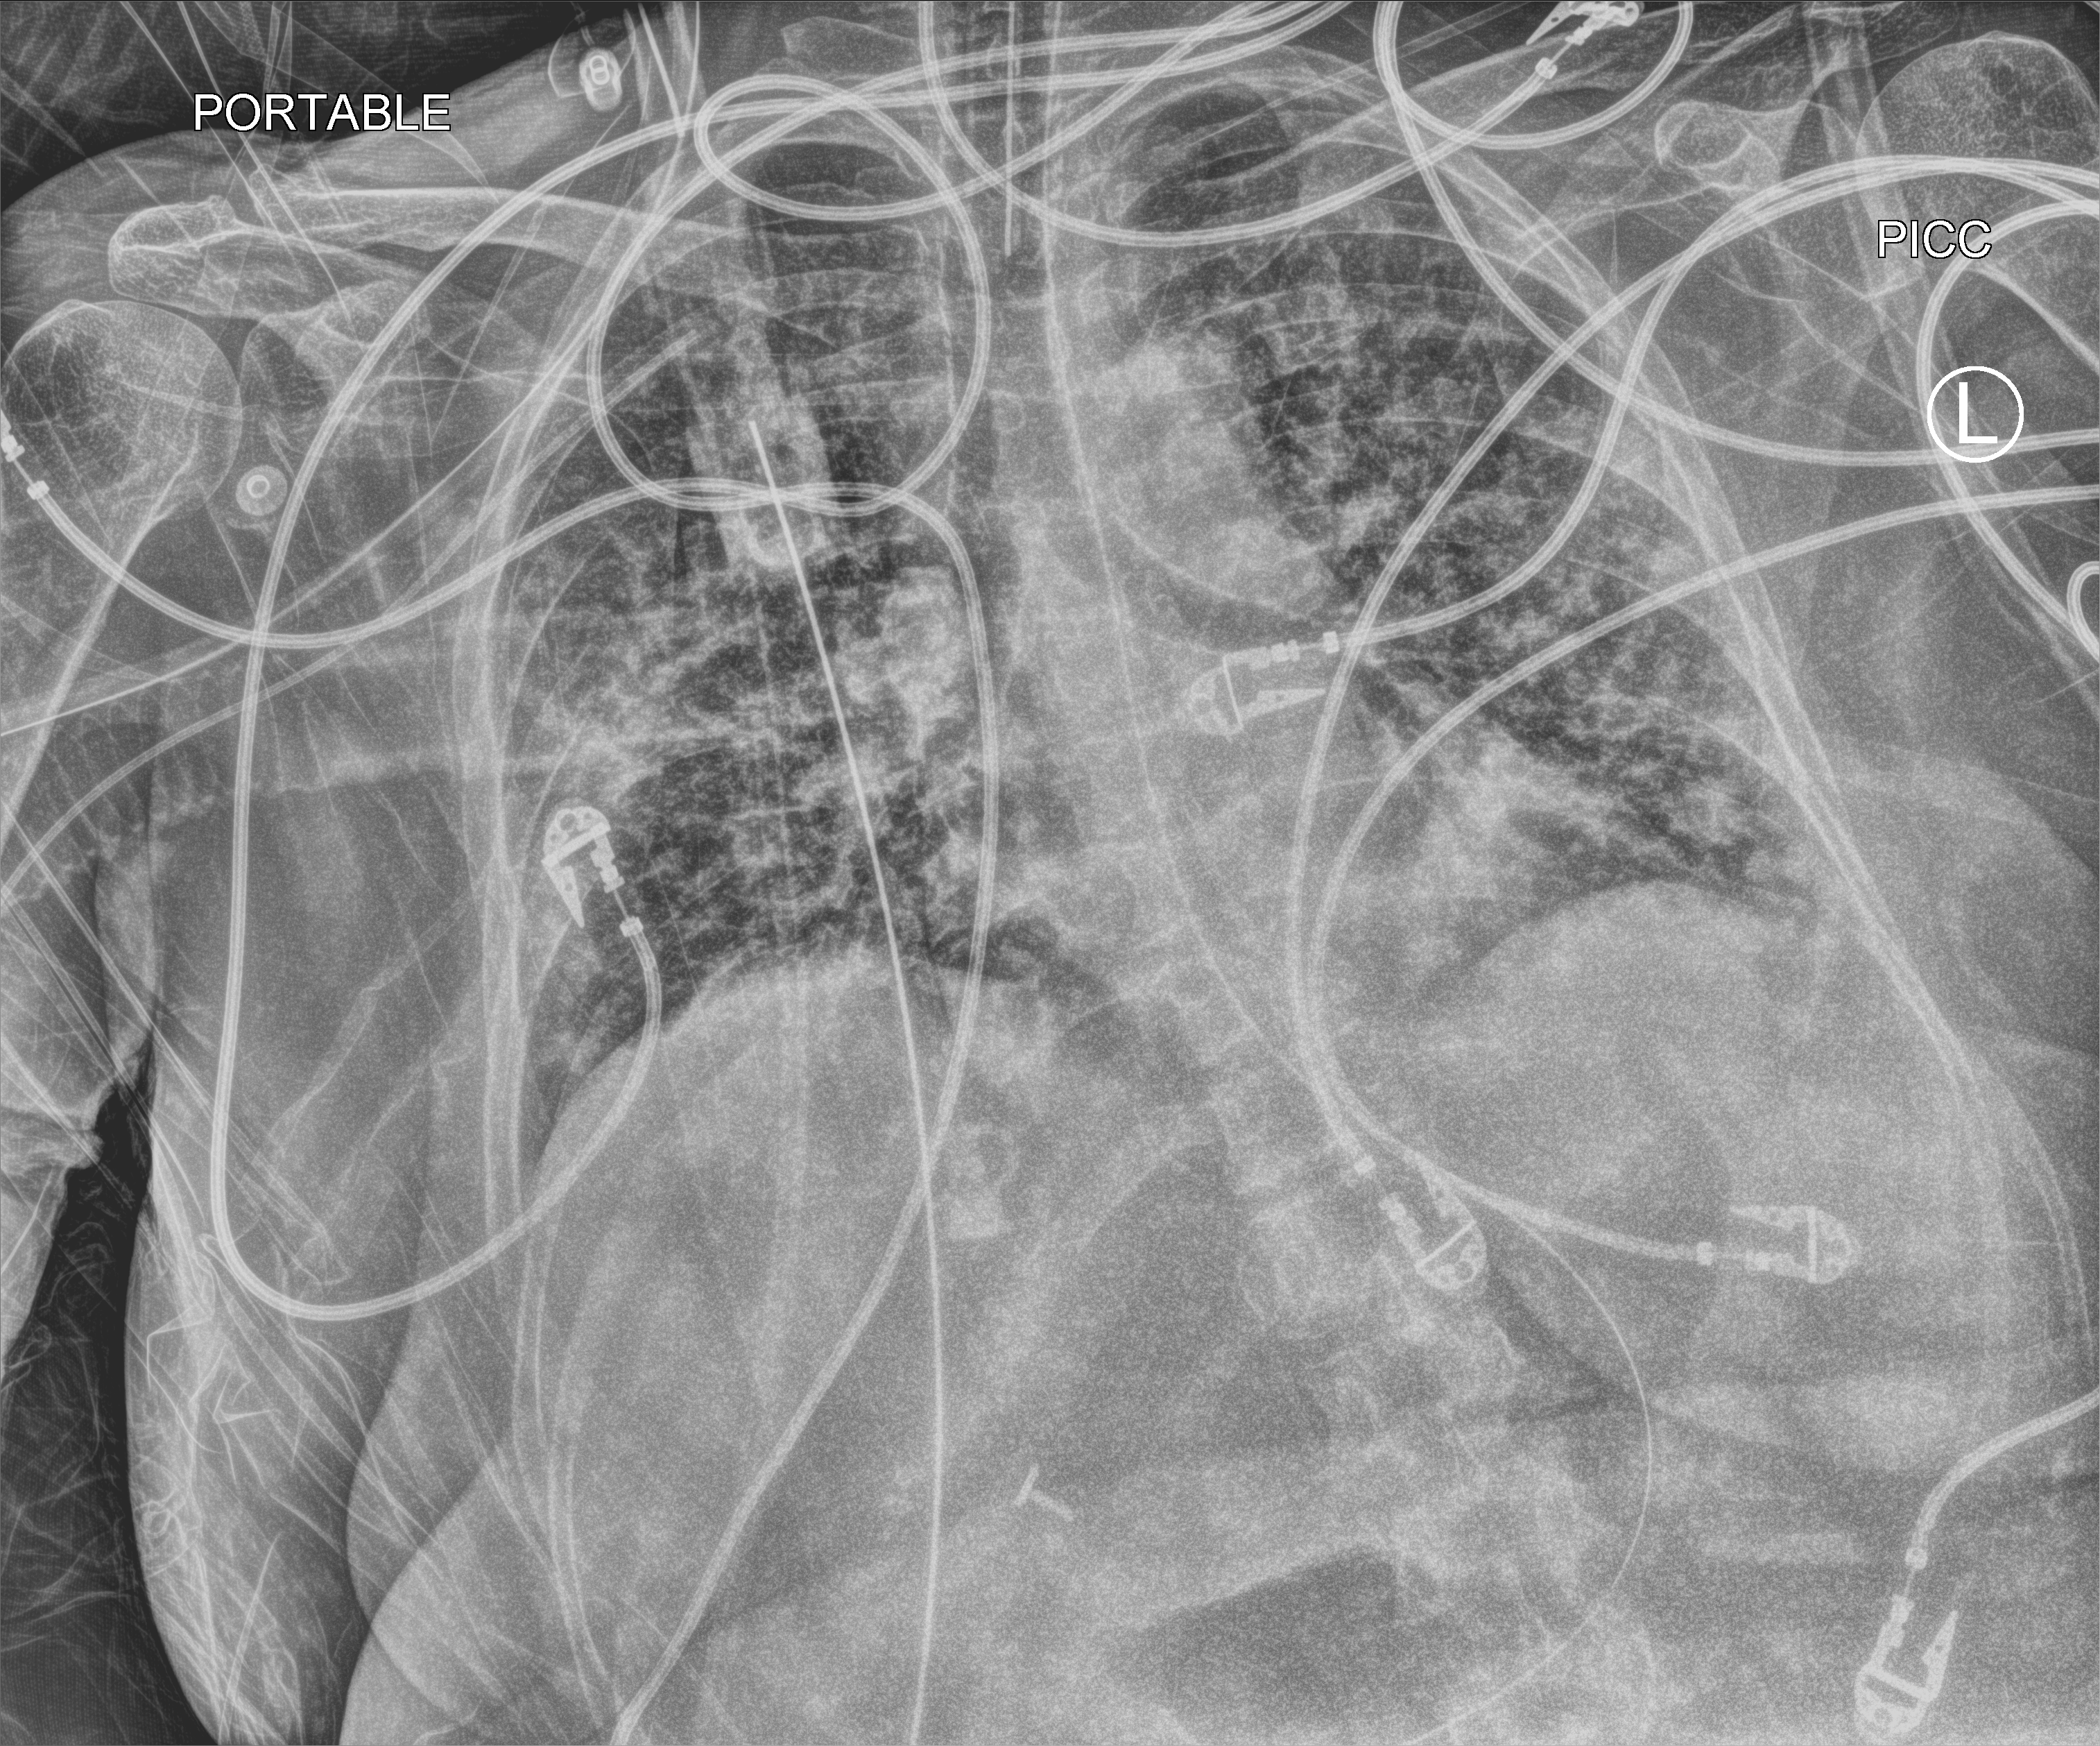
Bedside chest radiograph (computed radiography), anteroposterior (AP) projection. Patient hospitalised with COVID-19; female, aged 18–59 years.
Hospital-stay facts (about this admission, not read from this image; timing relative to this image not recorded):
- chronic kidney disease (admission record): yes
- length of hospital stay: 22 days
- admitted to intensive care during this hospital stay: yes